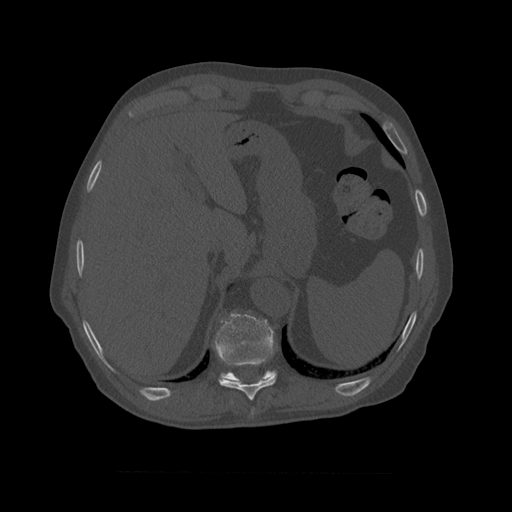
CT including the spine, one axial slice; slice 416 of 450 in the series (ordered by position); reconstruction kernel STANDARD; 120 kVp; bone window (W 1800 / L 400 HU); 1.25 mm slice thickness; 512 × 512 image matrix. Patient age 75 years. From the clinical record (not read from this slice): primary cancer: prostate.
Outlined on this slice (semi-automatic segmentation, software-assisted and operator-edited):
- T10 vertebra: bounding box <215,313,277,382> (left, top, right, bottom; pixels)
- T9 vertebra: <217,355,277,401>